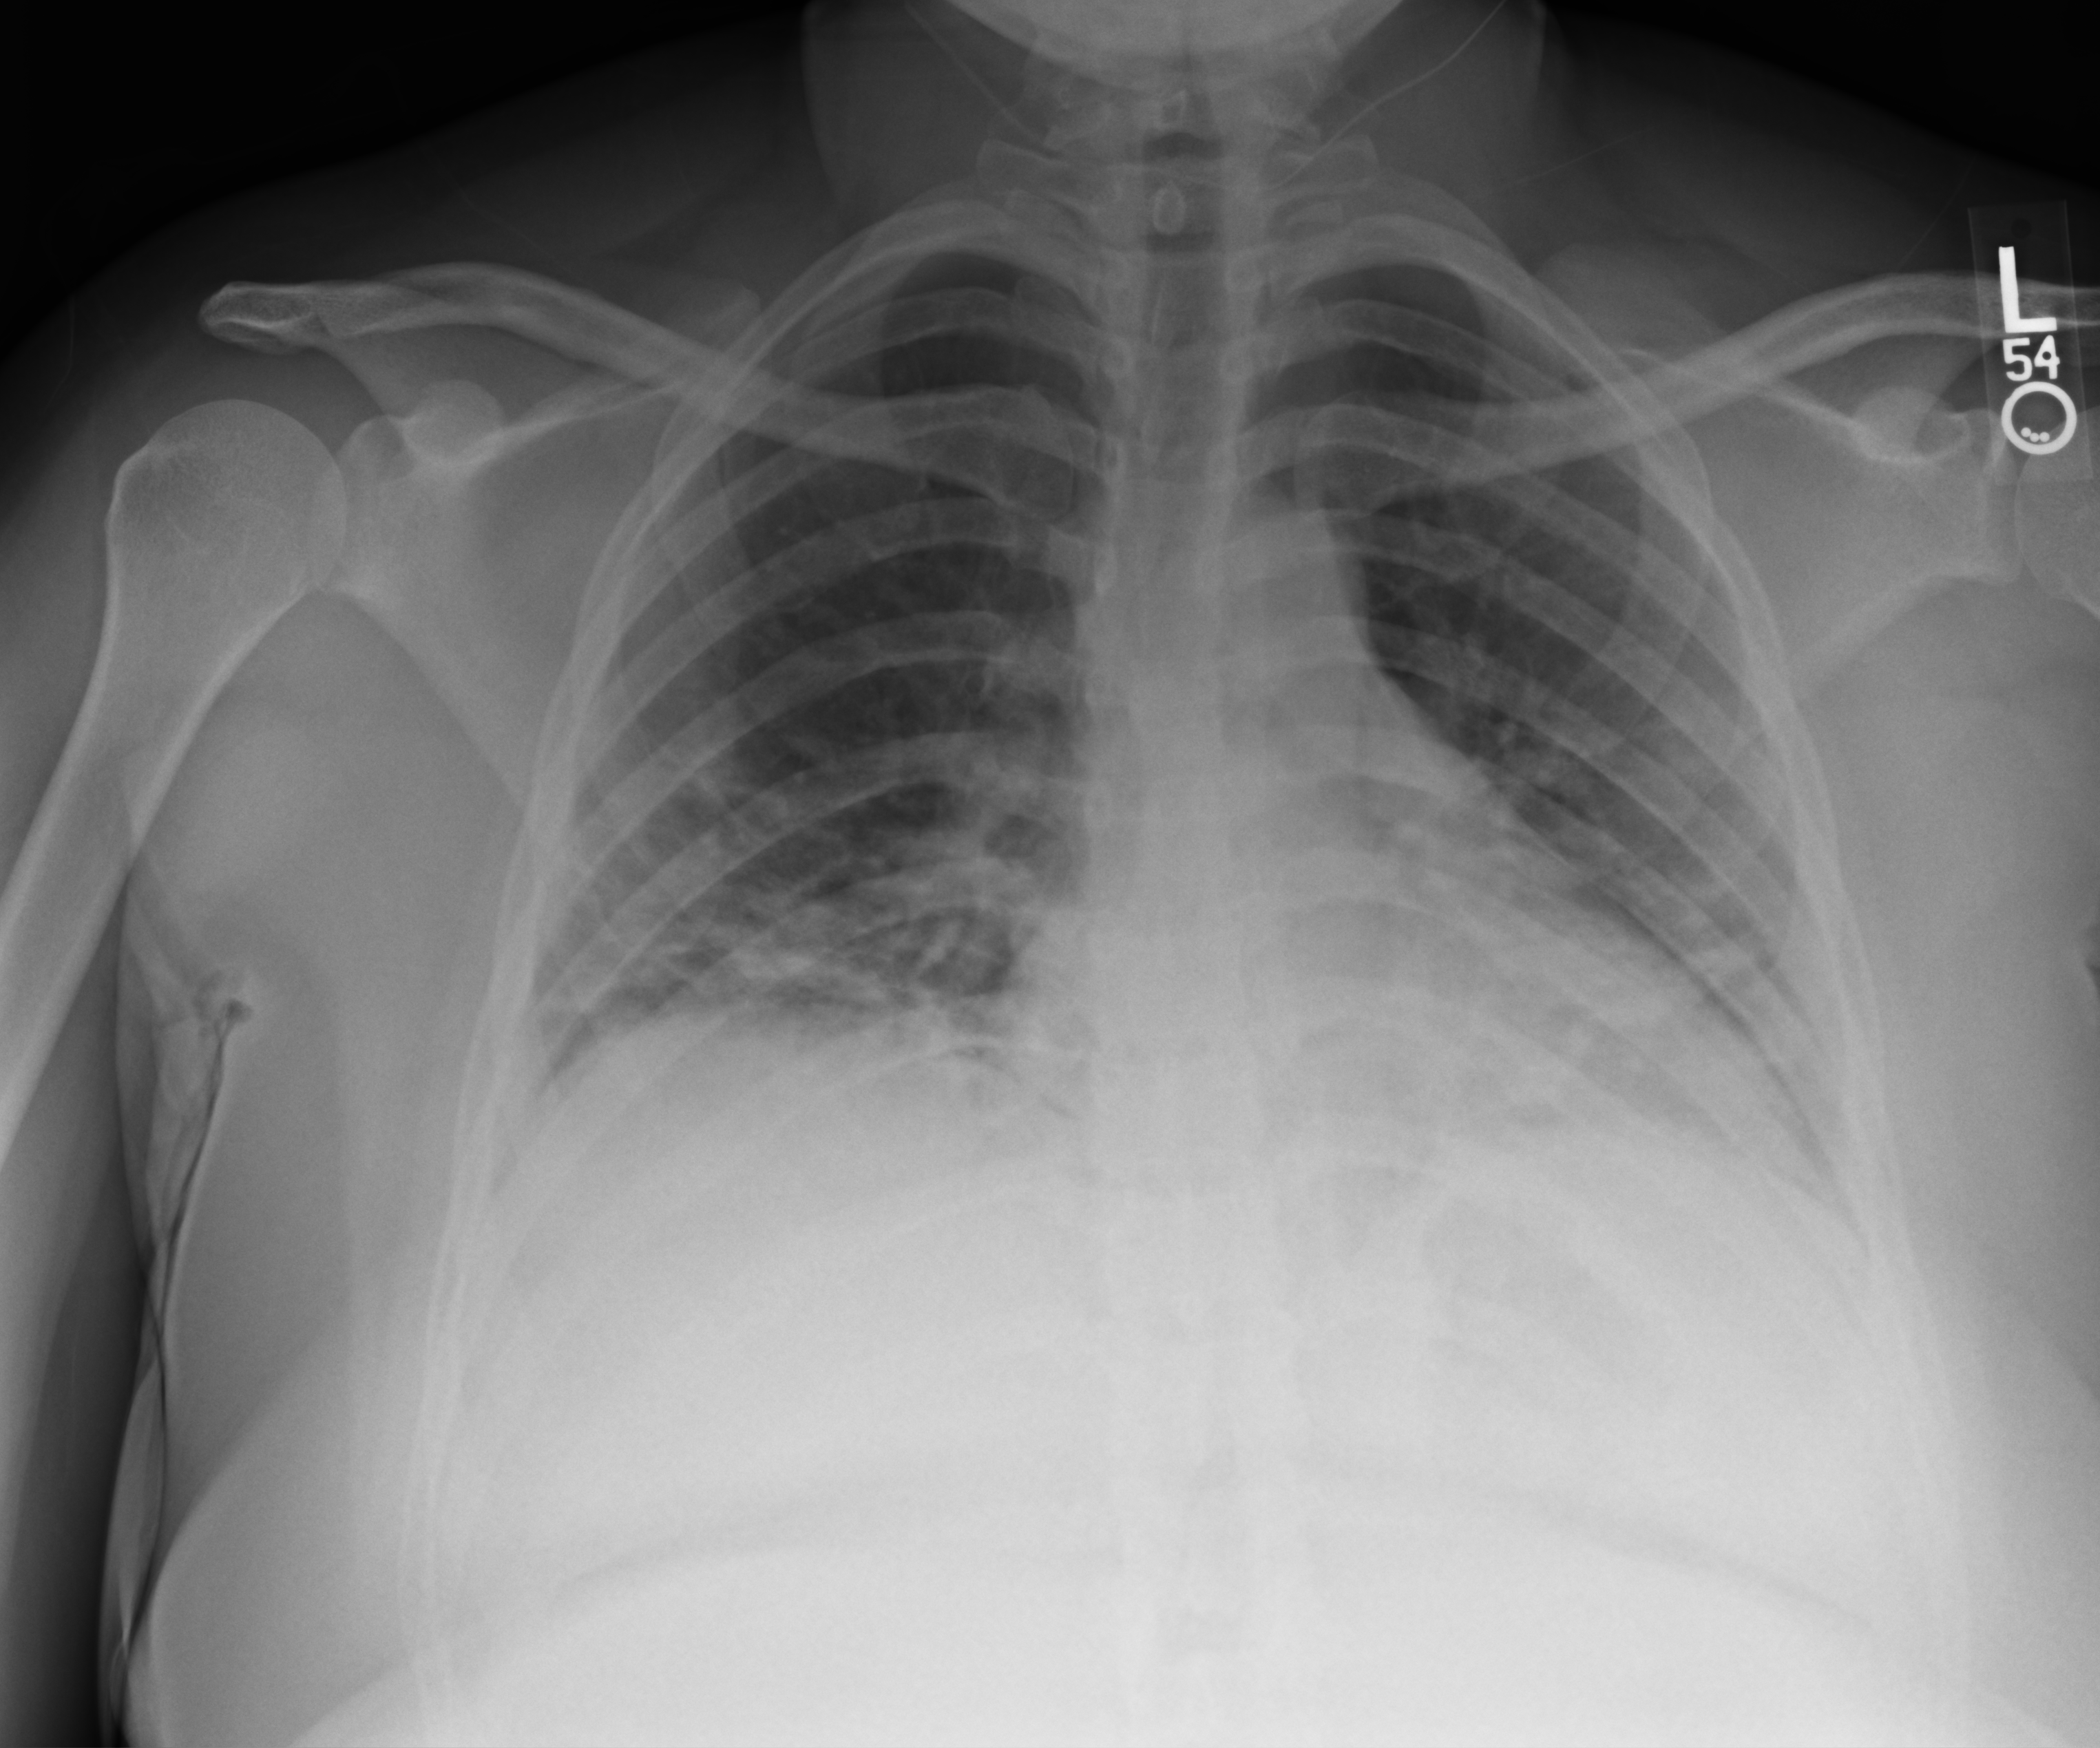
Portable chest radiograph, anteroposterior (AP) projection. Female patient hospitalised with COVID-19, age 18–59 years.
From the hospital-stay record, not from the radiograph (when in the stay this image was taken is not recorded): hypertension (admission record): no; COPD (admission record): no.